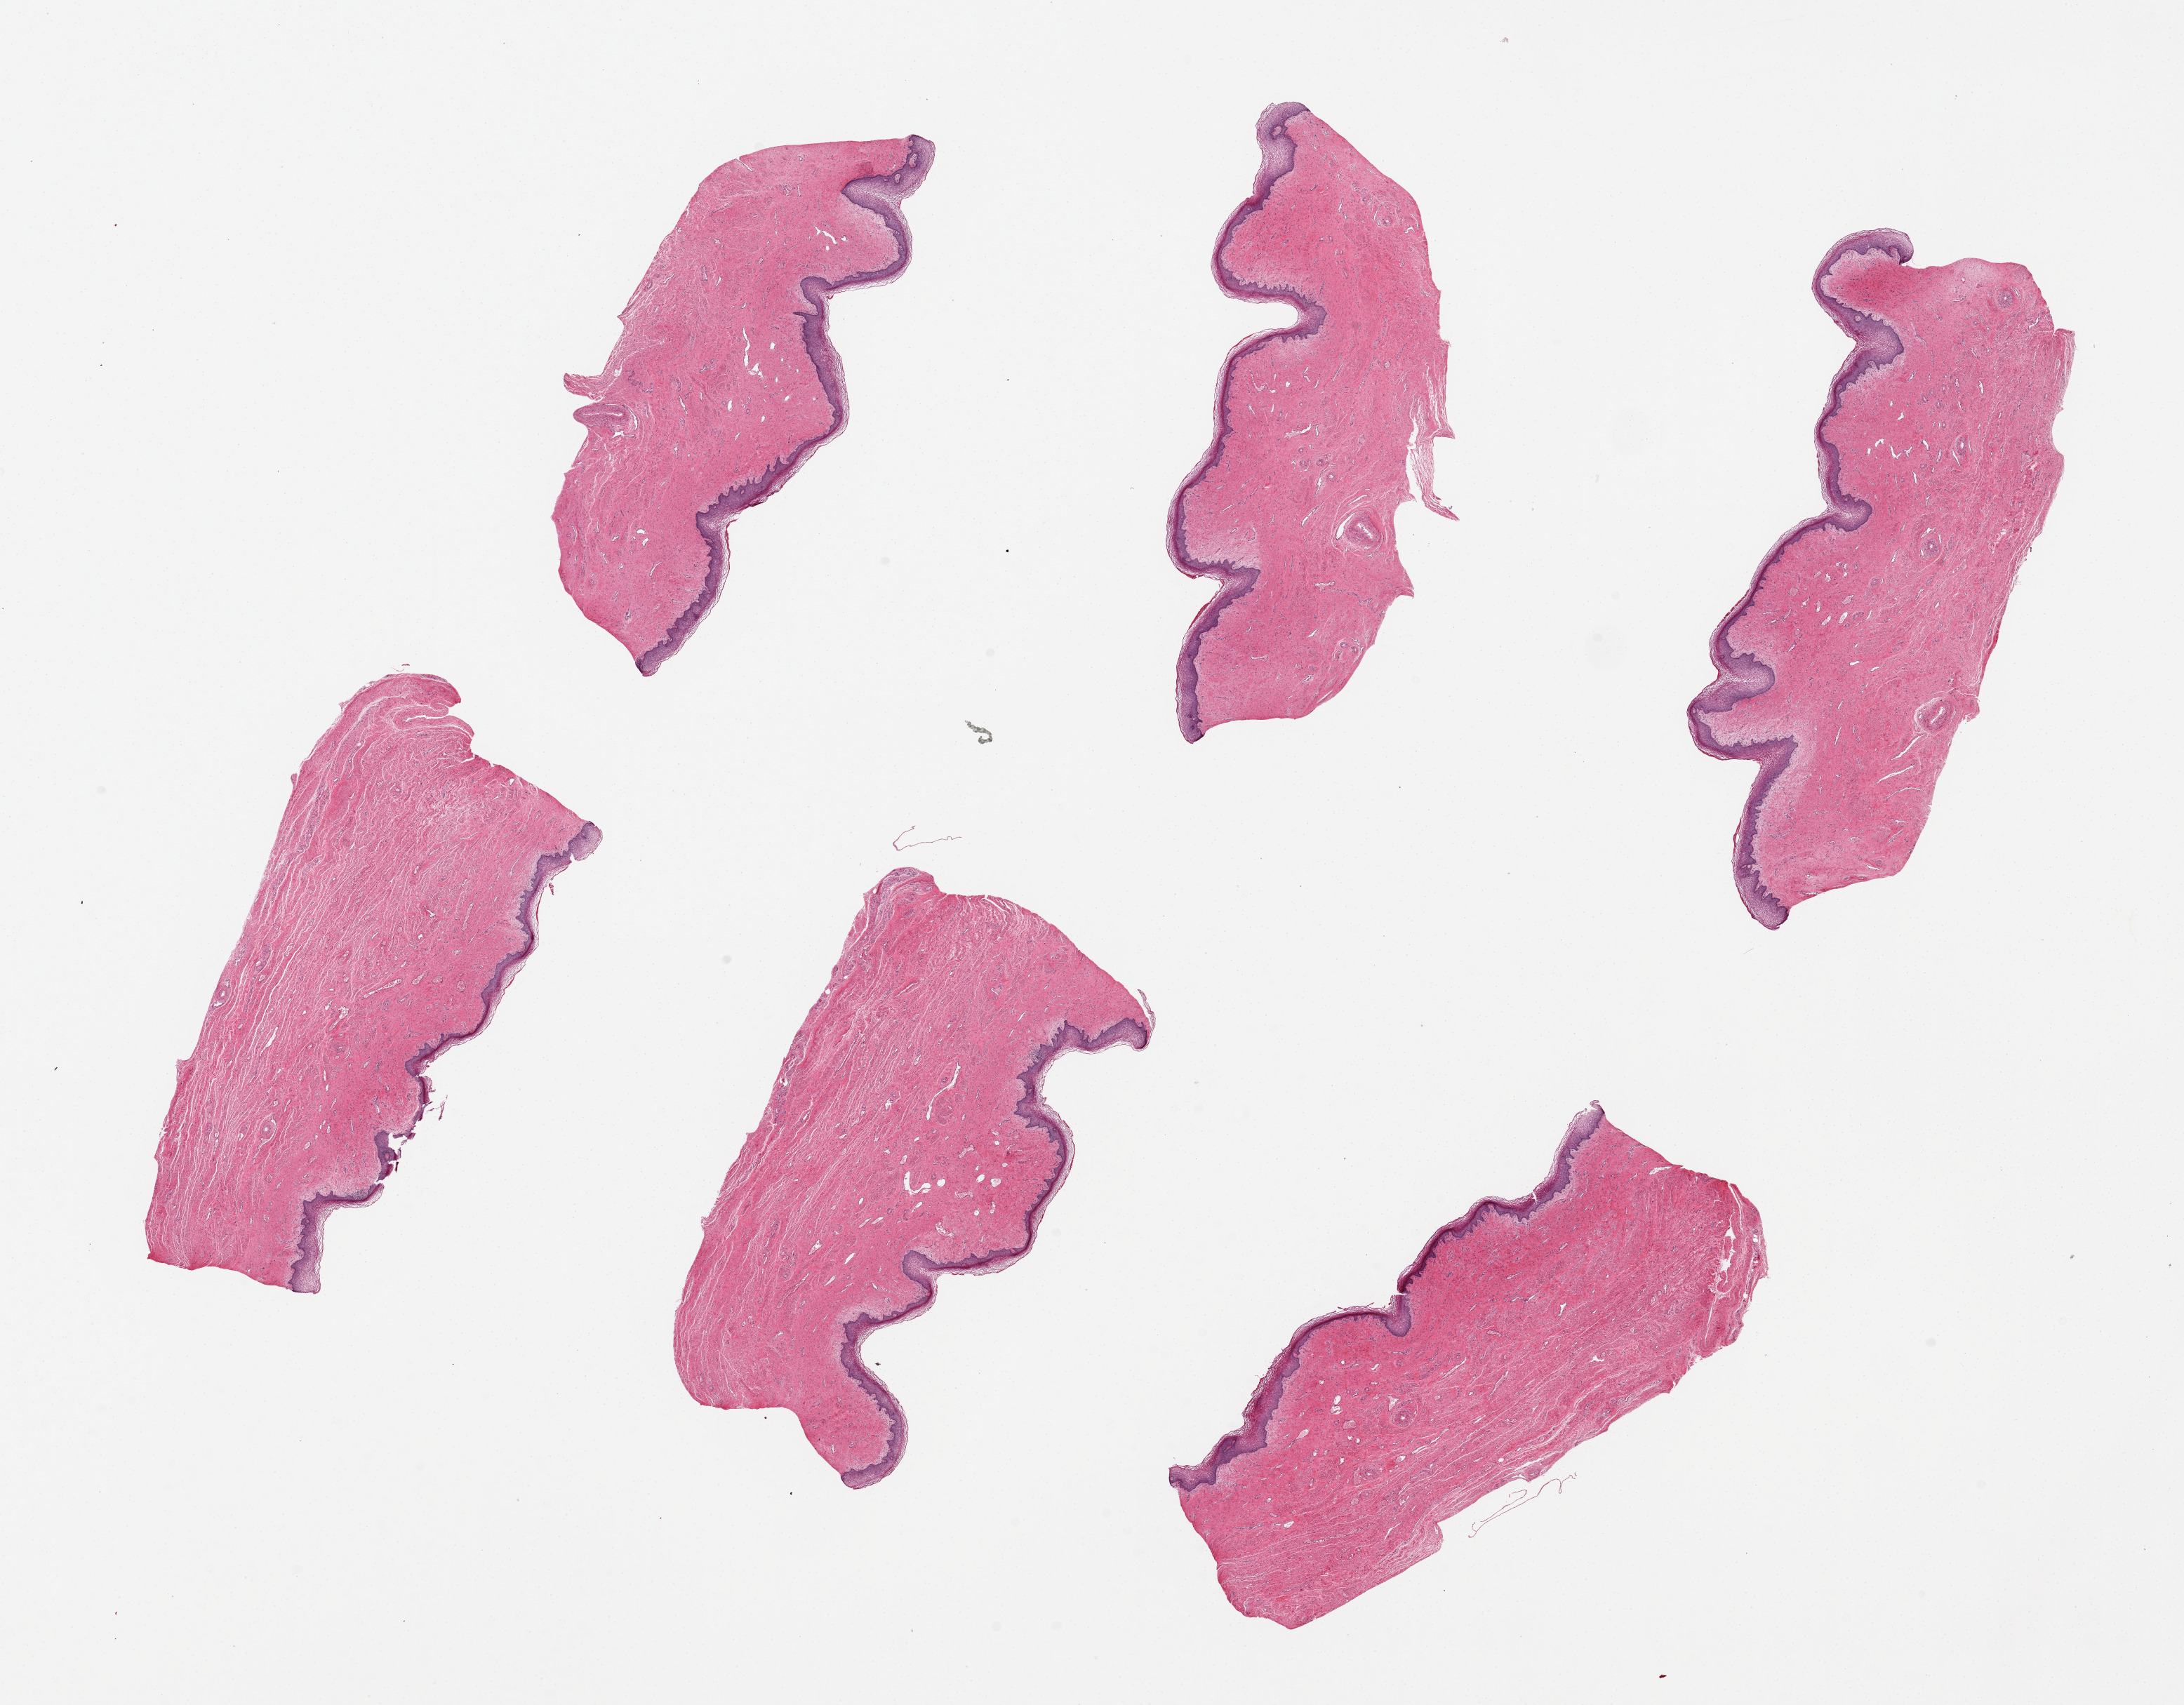
Whole-slide image, H&E stain, brightfield — a low-resolution overview of the entire scanned area, about 24.6 x 19.2 mm; PAXgene-fixed paraffin-embedded (PFPE) section; target tissue: vagina; donor tissue sample. Donor: female.
- pathologist's review note for this sample: 6 pieces, squamous epithelium is ~0.25mm thick